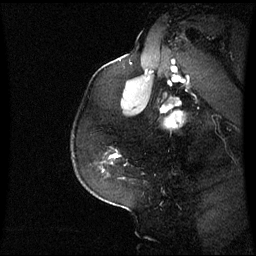
Breast MRI (dynamic contrast-enhanced), one sagittal slice. Slice 47 of 60 in the series (ordered by position). Dynamic contrast-enhanced series, image 2 of 3 at this slice position (ordered by acquisition). 1.5 T. TE 4.2 ms, TR 8.9 ms. 2.4 mm slice thickness. 256 × 256 image matrix, field of view 230 × 230 mm. Patient: female, 59 years. From the clinical record (not read from this slice): setting: breast cancer imaged before/during neoadjuvant chemotherapy; receptor status: triple-negative.
Annotated regions visible in this slice (semi-automatically segmented with operator editing):
- analysis volume of interest (the breast-tissue region the enhancement analysis was run in; not a lesion): bounding box (x1, y1, x2, y2) in pixels: (110, 150, 119, 164)
- tumour enhancement mask (voxels above the 70 % enhancement threshold inside the analysis volume of interest): (111, 155, 118, 158)